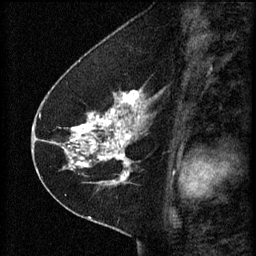
Breast MRI (dynamic contrast-enhanced), one sagittal slice. Position 27 of 60 along the scan axis. 3 images stored at this slice position (order not interpretable as contrast timing). 1.5 T. TE 4.2 ms, TR 8.2 ms. 2 mm slice thickness. 256 × 256 image matrix, field of view 180 × 180 mm. Female patient, age 41 years.
Structures marked on this image (semi-automatically segmented with operator editing):
- analysis volume of interest (the breast-tissue region the enhancement analysis was run in; not a lesion): bounding box <67,92,165,173> (left, top, right, bottom; pixels)
- tumour enhancement mask (voxels above the 70 % enhancement threshold inside the analysis volume of interest): <67,92,143,173>